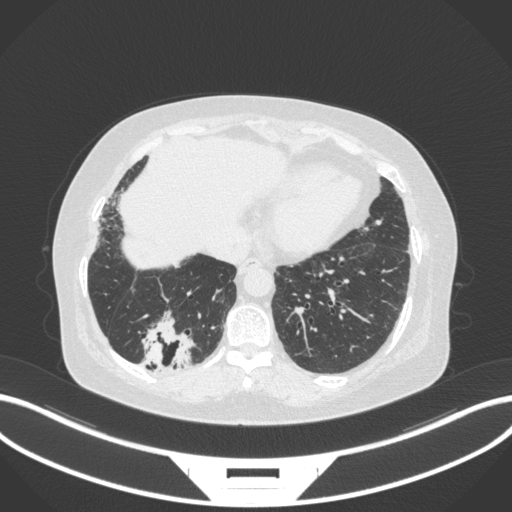
Chest CT, one axial slice. Position 50 of 303 along the scan axis. 120 kVp. Lung window (W 1500 / L -600 HU). 512 × 512 image matrix, field of view 400 × 400 mm. Patient: female, 65 years. Case-level facts recorded for this patient, not image findings: clinical TNM (as recorded): T2b N1 M0.
Annotated regions visible in this slice (rectangle marked by the reading radiologist):
- lung tumour (recorded histology: adenocarcinoma): bounding box [x1, y1, x2, y2] px = [133, 310, 198, 374]